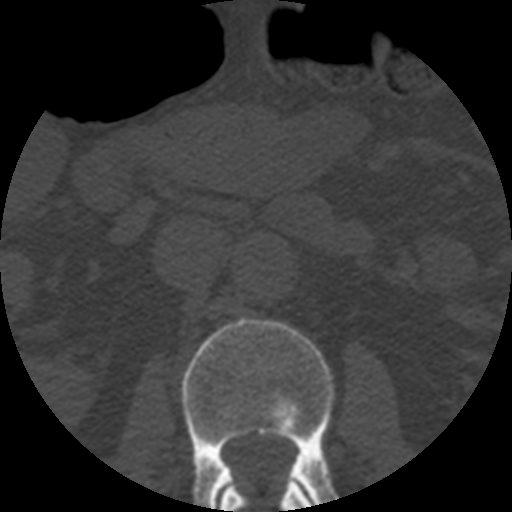
CT including the spine, one axial slice; position 161 of 508 along the scan axis; reconstruction kernel STANDARD; 120 kVp; bone window (W 1800 / L 400 HU); 512 × 512 image matrix, field of view 160 × 160 mm. Patient age 57 years. Case-level facts recorded for this patient, not image findings: primary cancer: prostate.
Structures marked on this image (semi-automatic segmentation, software-assisted and operator-edited):
- L1 vertebra: box from (x=220, y=482) to (x=314, y=512) px
- L2 vertebra: (x=181, y=319)–(x=336, y=512)